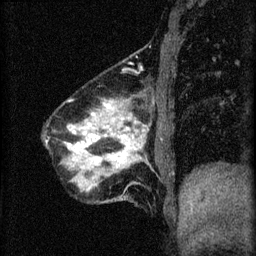
Breast MRI (dynamic contrast-enhanced), one sagittal slice. Position 15 of 60 along the scan axis. 3 images stored at this slice position (order not interpretable as contrast timing). 1.5 T. TE 4.2 ms, TR 8.2 ms. 2 mm slice thickness. 256 × 256 image matrix. Patient: female, 40 years.
Outlined on this slice (semi-automatically segmented with operator editing):
- analysis volume of interest (the breast-tissue region the enhancement analysis was run in; not a lesion): bounding box <46,94,173,203> (left, top, right, bottom; pixels)
- tumour enhancement mask (voxels above the 70 % enhancement threshold inside the analysis volume of interest): <64,102,141,169>